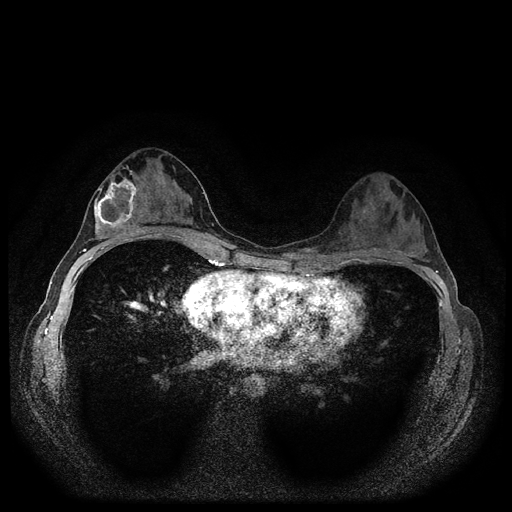
Breast MRI (dynamic contrast-enhanced, multi-phase), one axial slice. Slice 58 of 116 in the series (ordered by position). Dynamic contrast-enhanced series, time point 2 of 5 at this slice position (early post-contrast). 1.5 T. TE 2.7 ms, TR 5.4 ms. 2 mm slice thickness. 512 × 512 image matrix. Patient: female, 29 years.
Structures marked on this image (semi-automatically segmented with operator editing):
- breast lesion (labelled 'tumour' in the annotation; benign lesions carry a separate 'benign' label): box from (x=89, y=180) to (x=139, y=241) px